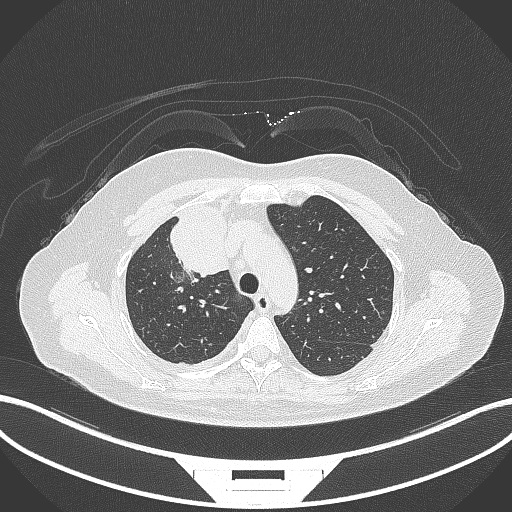
Chest CT, one axial slice. Position 222 of 305 along the scan axis. 120 kVp. Lung window (W 1500 / L -600 HU). 512 × 512 image matrix, field of view 400 × 400 mm. Patient: female, 52 years. Case-level facts recorded for this patient, not image findings: clinical TNM (as recorded): T3 N1 M1.
Outlined on this slice (bounding box drawn by a radiologist):
- lung tumour (recorded histology: adenocarcinoma): bounding box [x1, y1, x2, y2] px = [165, 199, 233, 279]